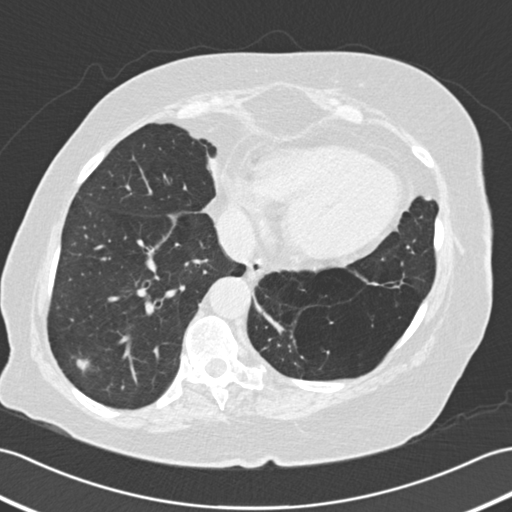
Low-dose screening chest CT, one axial slice. Slice 57 of 161 in the series (ordered by position). Reconstruction kernel B30f. Lung window (W 1500 / L -600 HU). 2 mm slice thickness. 512 × 512 image matrix, field of view 353 × 353 mm.
Structures marked on this image (manually delineated by an expert):
- lesion 1 (tumor, lower lobe of right lung): bounding box (x1, y1, x2, y2) in pixels: (77, 359, 89, 371)